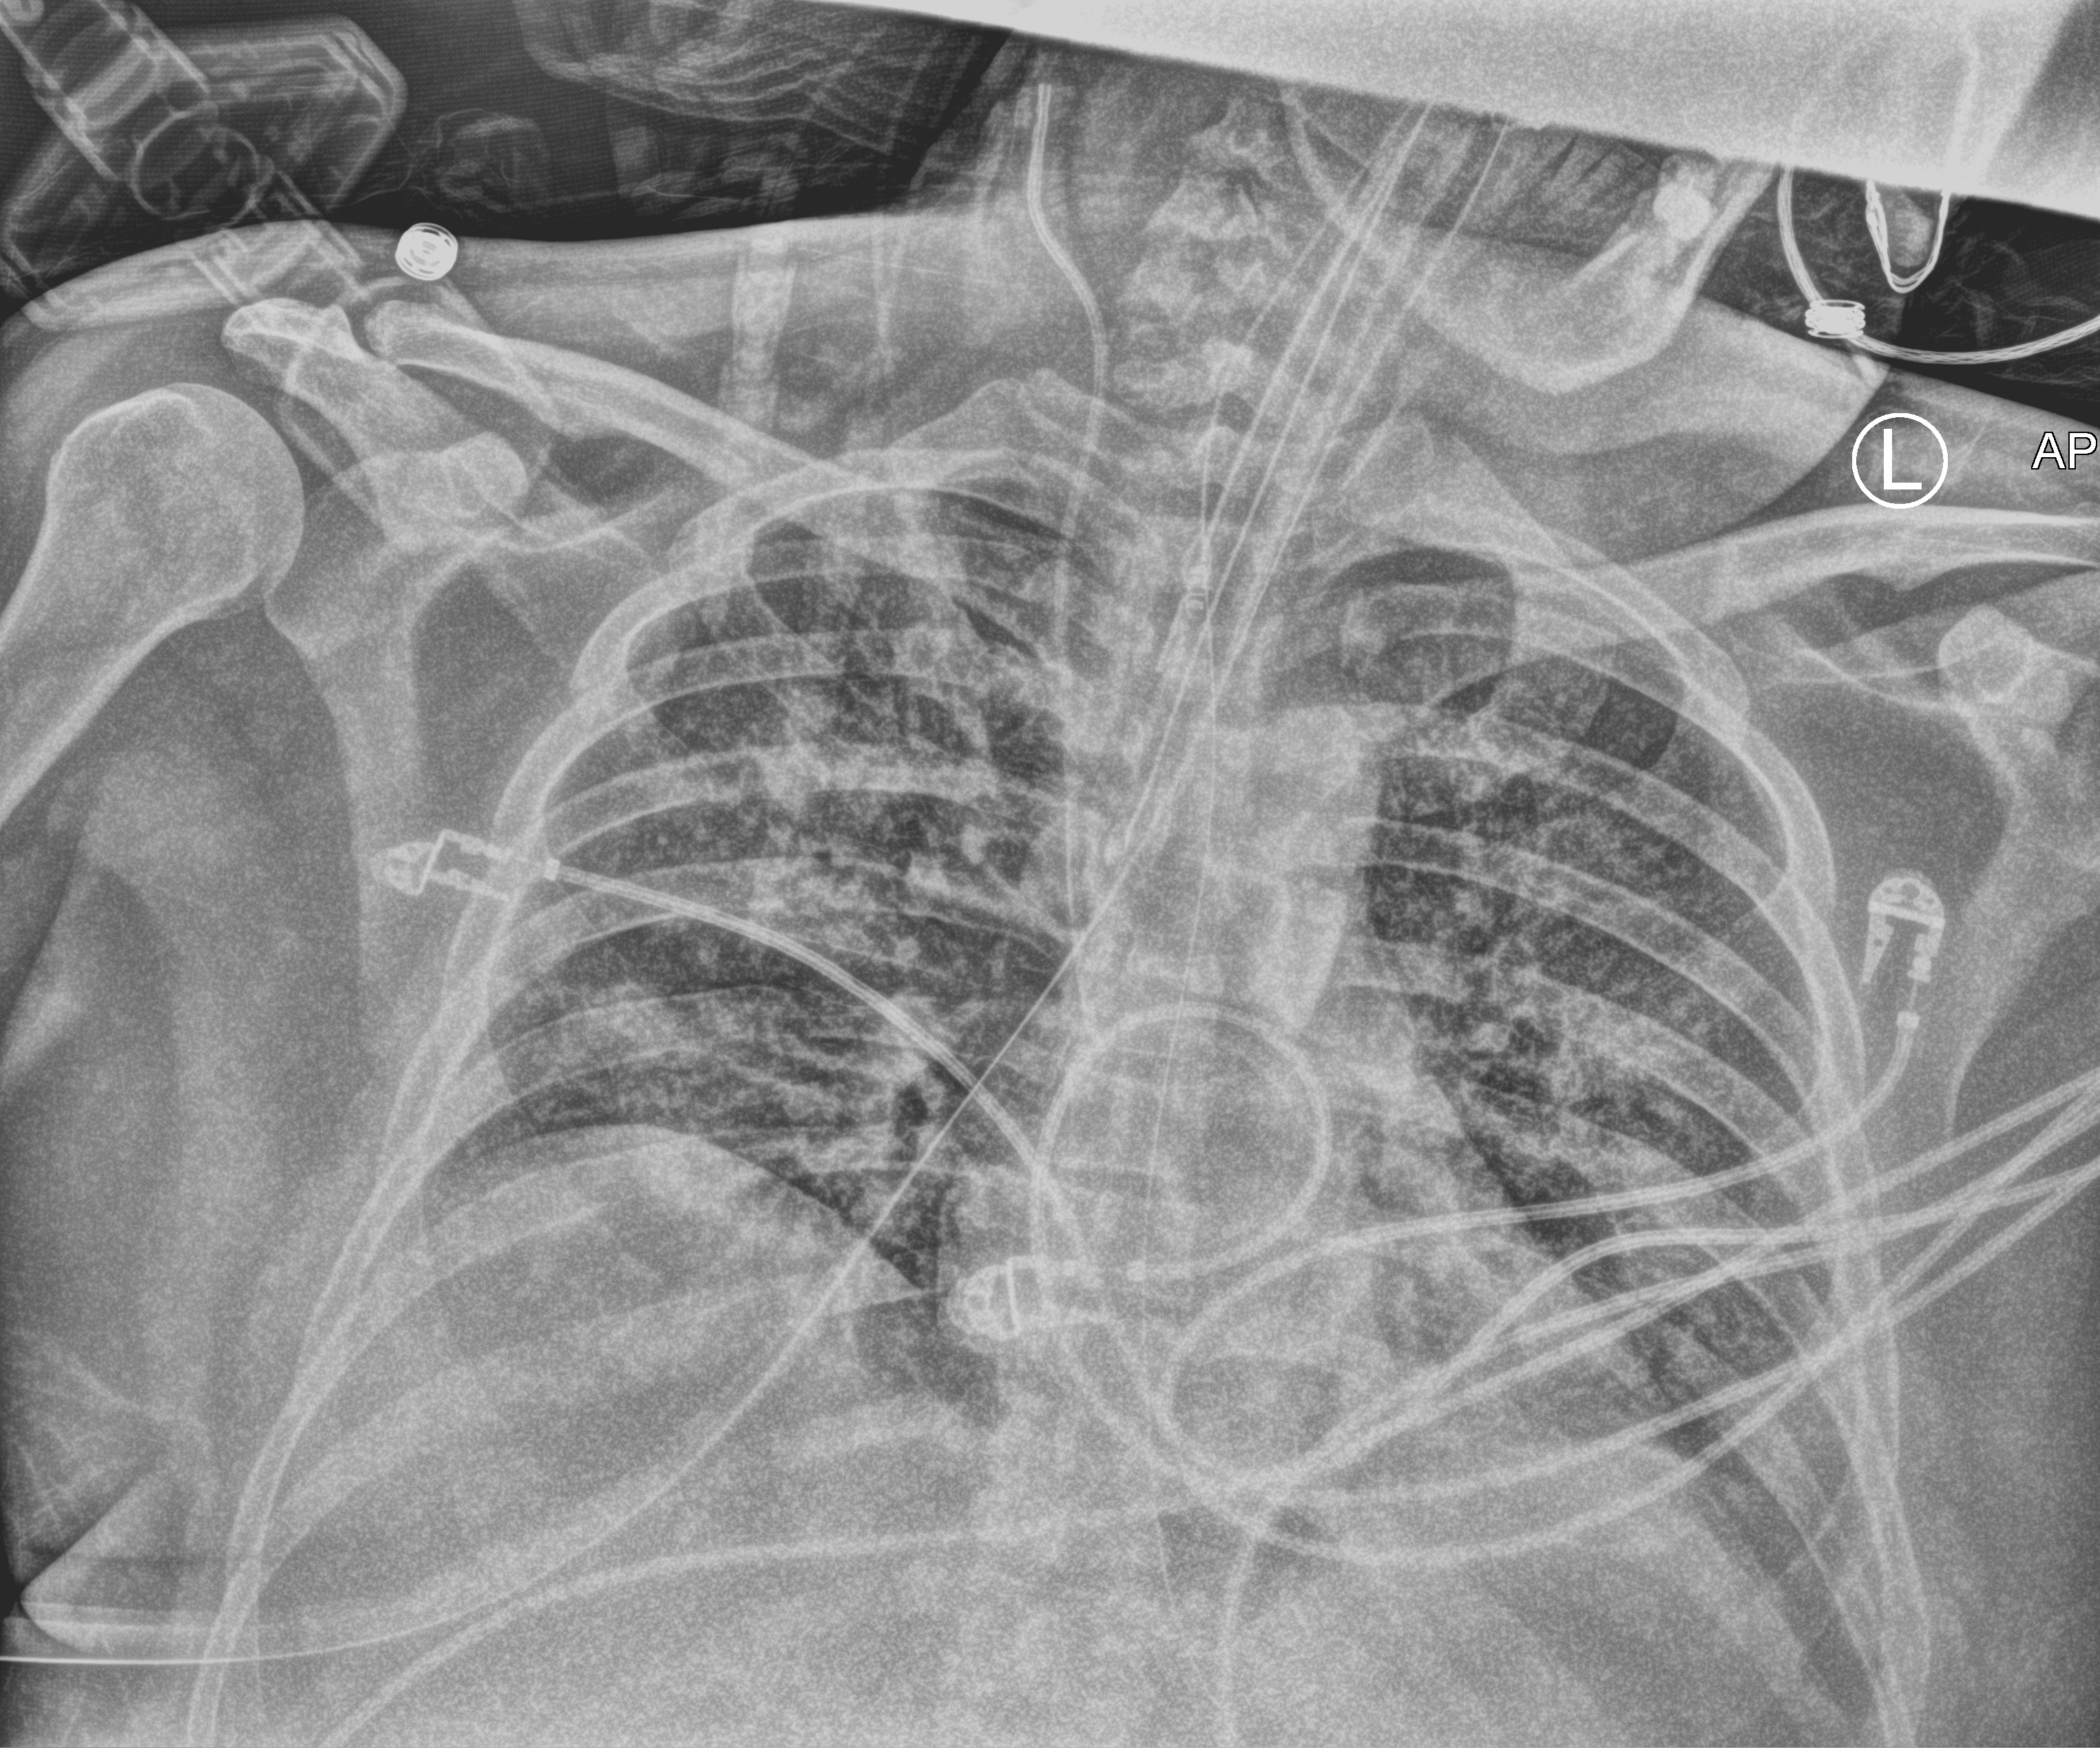
Bedside chest radiograph (computed radiography). Male patient hospitalised with COVID-19, age 18–59 years.
Admission-level facts for this patient (not findings on this image; timing relative to this image not recorded):
- chronic kidney disease (admission record): no